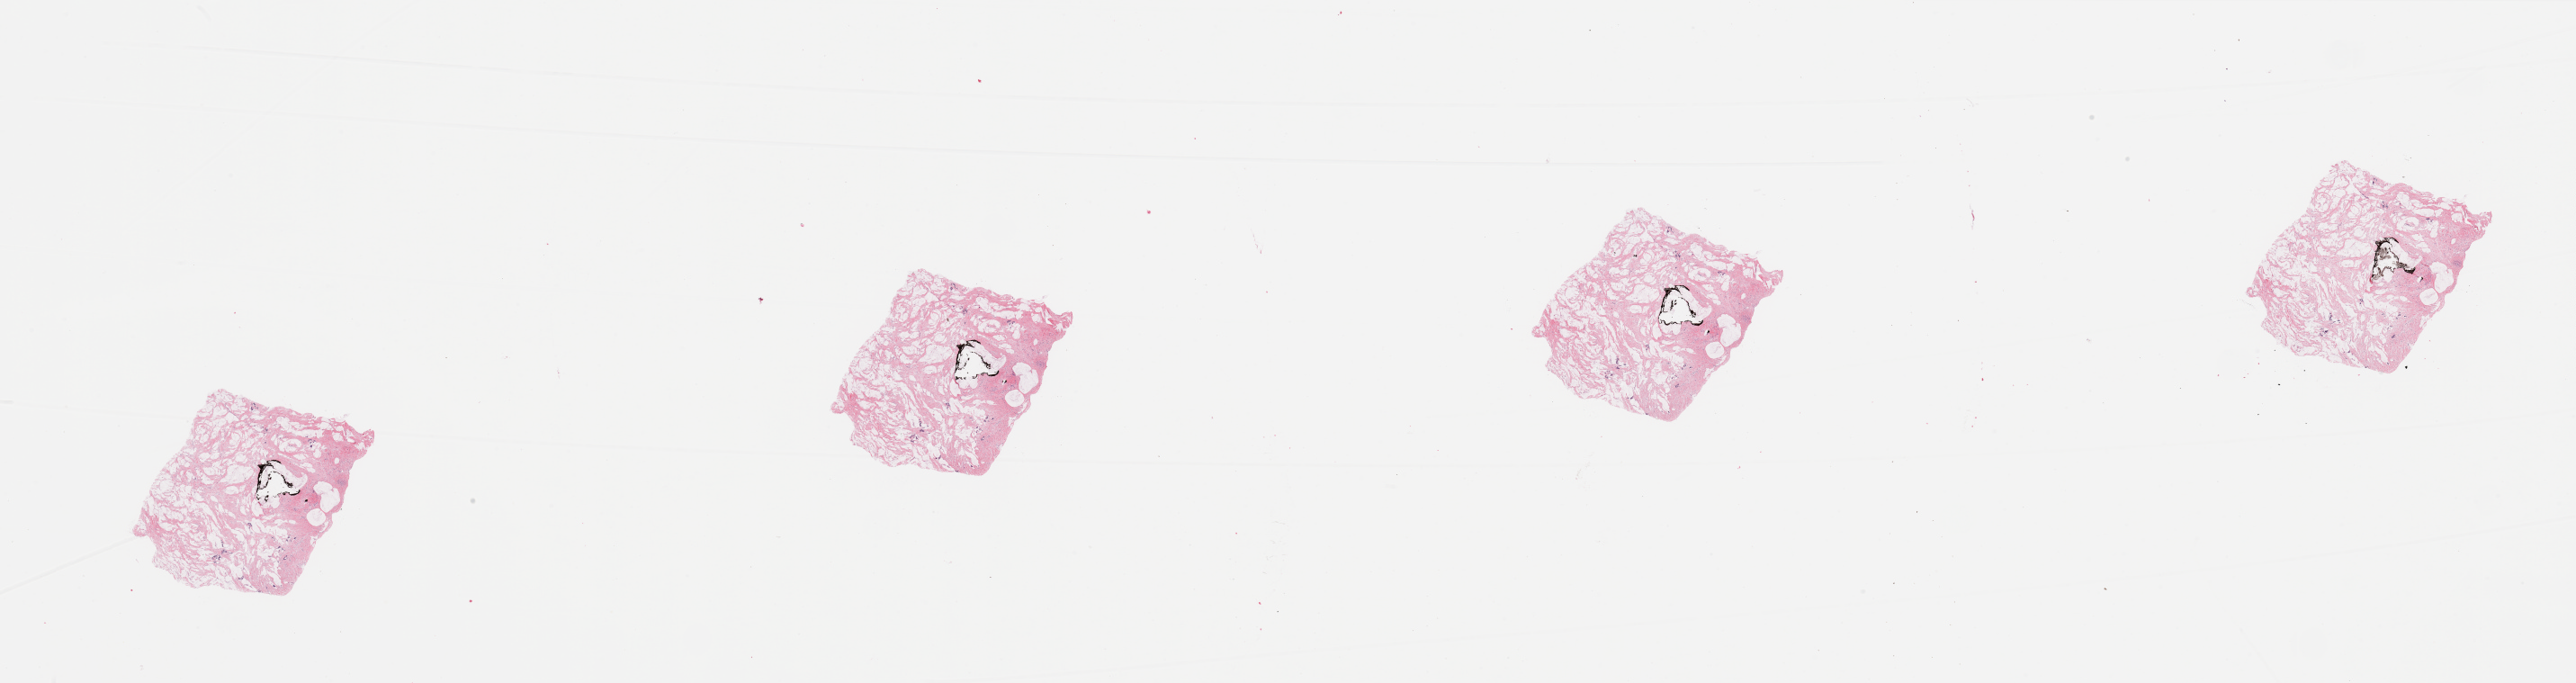
Whole-slide histology image, Hematoxylin and eosin (H&E) stained, whole scanned area (about 45.3 x 12.0 mm, slide scanned at 20x) shown as a low-resolution overview, tumour tissue sample, pancreas. Male, 63 y/o.
Patient diagnosis (cohort enrolment): ductal adenocarcinoma (pancreas). Primary tumour site (as recorded): head.